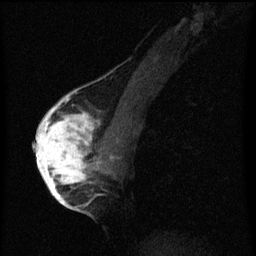
Breast MRI (dynamic contrast-enhanced), one sagittal slice; position 32 of 60 along the scan axis; dynamic contrast-enhanced series, image 2 of 3 at this slice position (ordered by acquisition); 1.5 T; TE 4.2 ms, TR 8 ms; 2 mm slice thickness; 256 × 256 image matrix, field of view 180 × 180 mm. Female patient, age 56 years.
Annotated regions visible in this slice (semi-automatically segmented with operator editing):
- analysis volume of interest (the breast-tissue region the enhancement analysis was run in; not a lesion): box from (x=42, y=110) to (x=107, y=193) px
- tumour enhancement mask (voxels above the 70 % enhancement threshold inside the analysis volume of interest): (x=42, y=110)–(x=95, y=193)